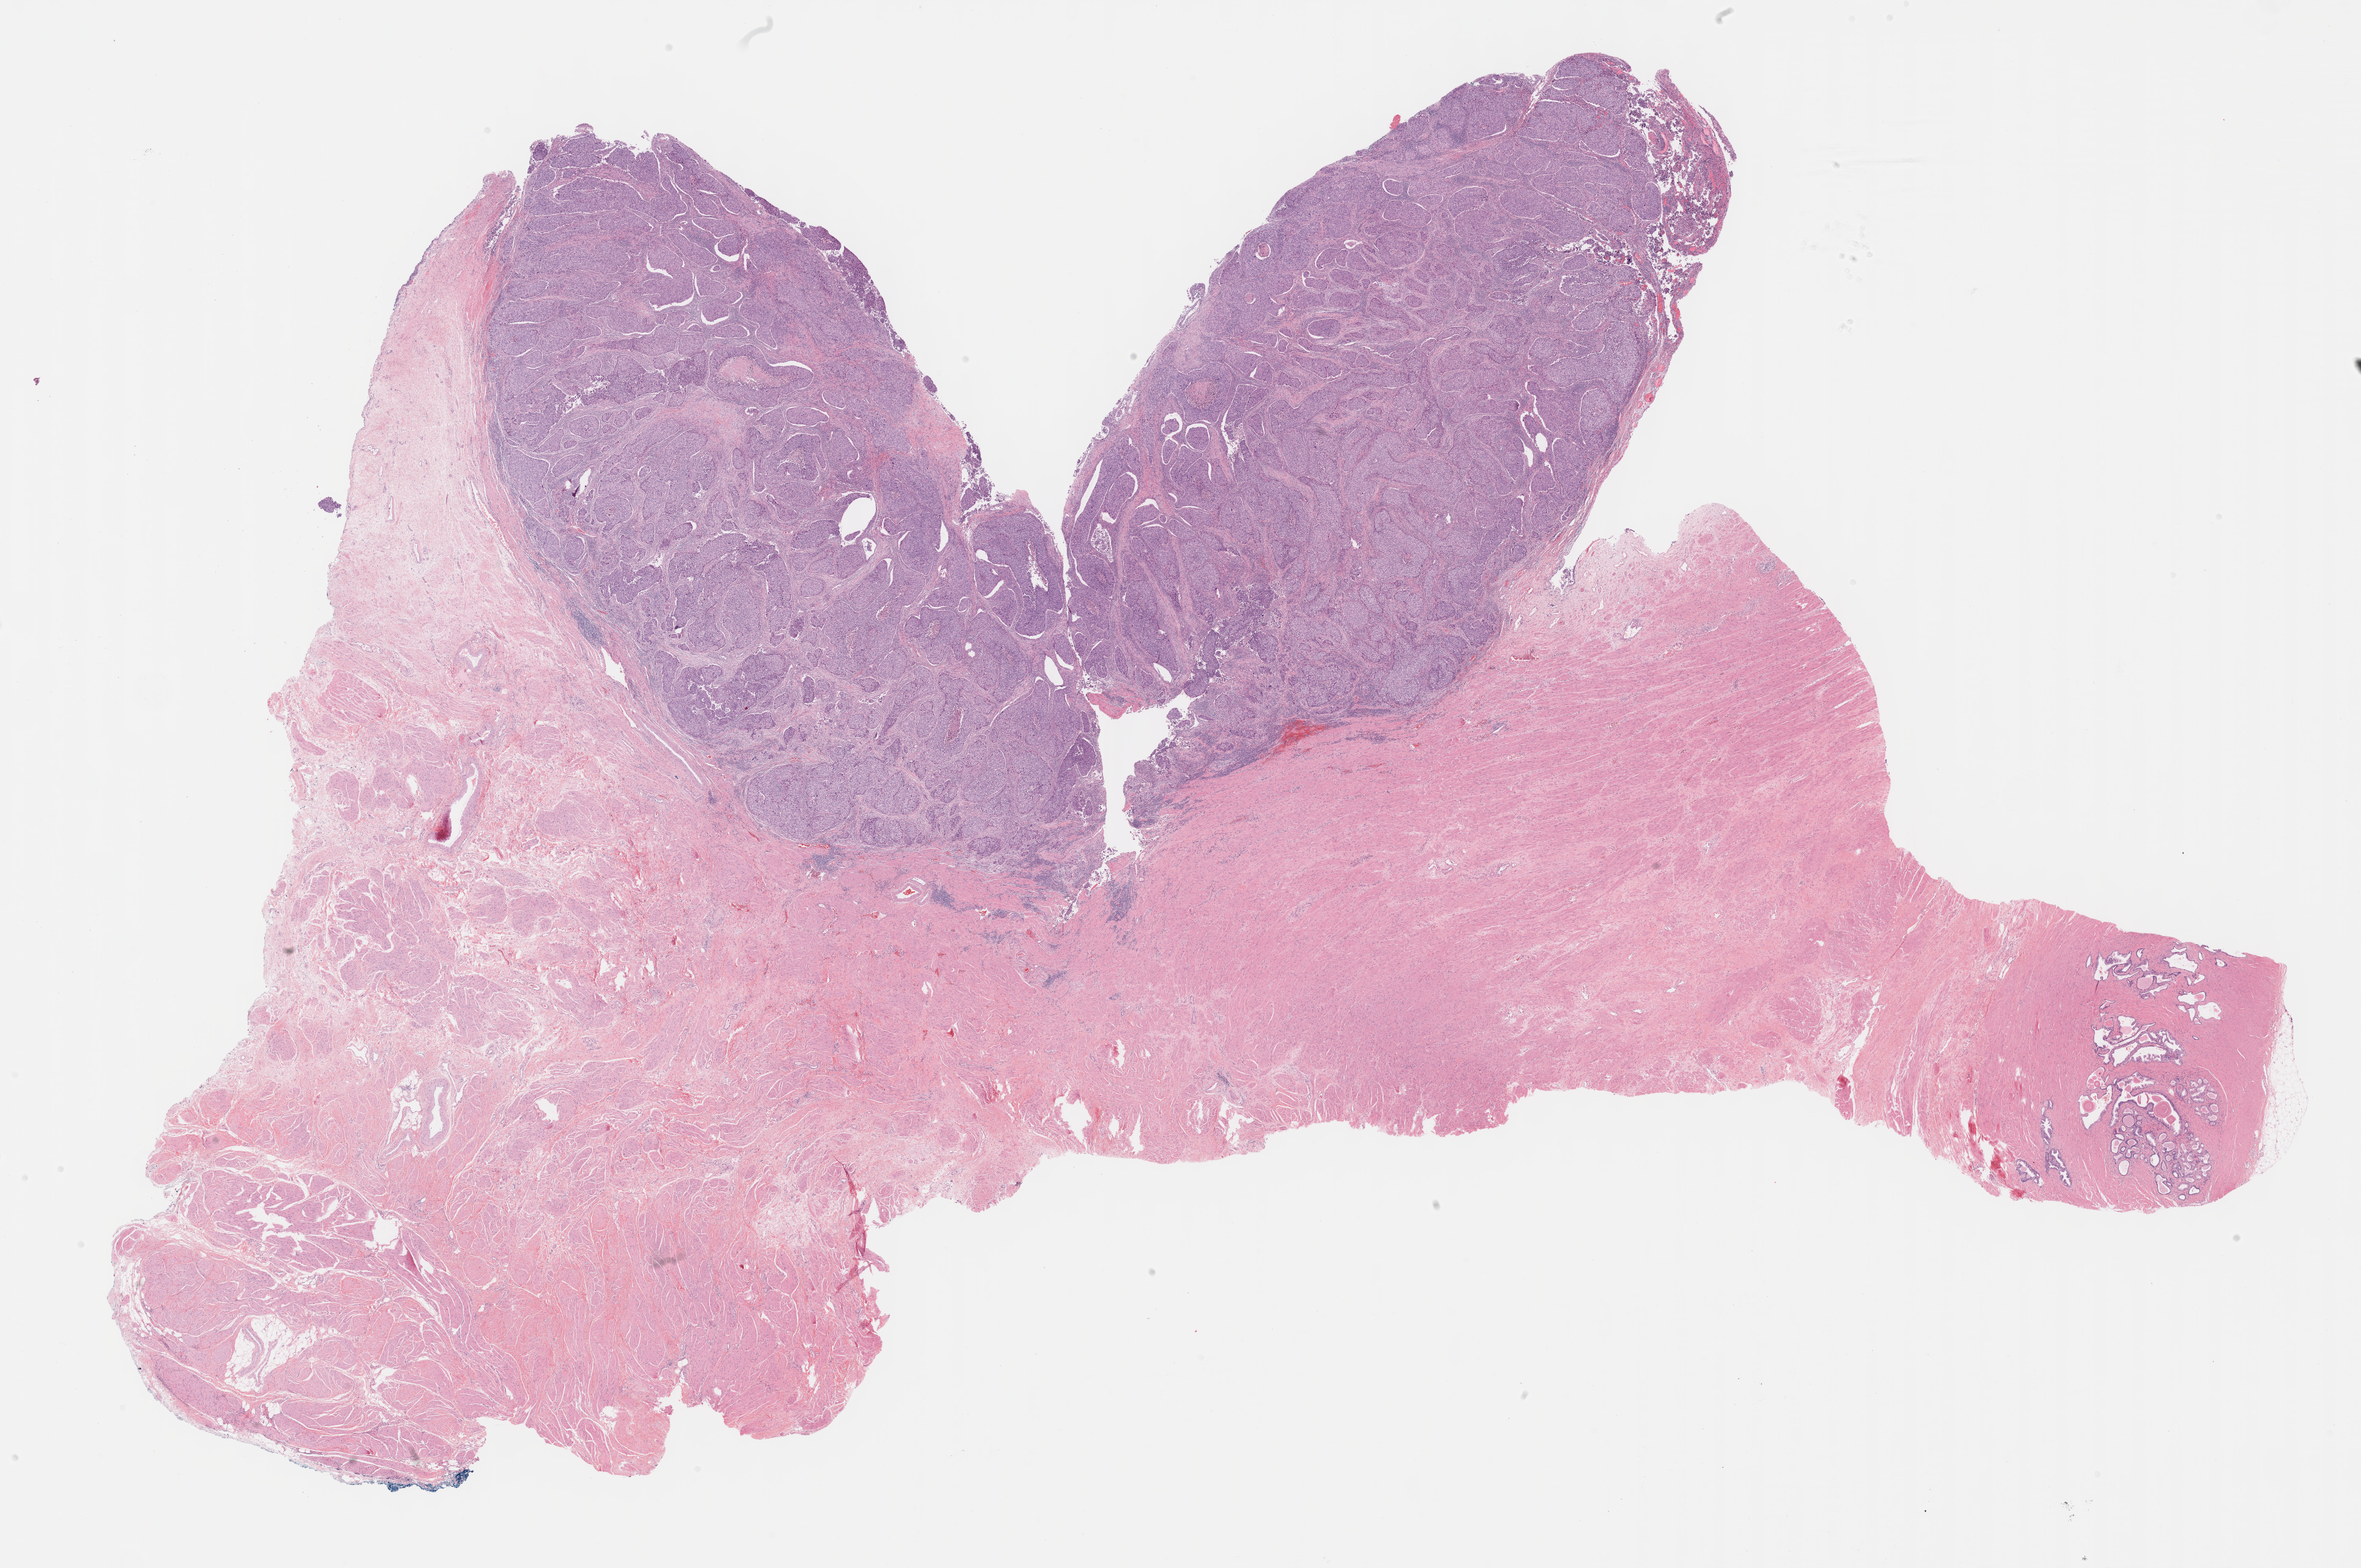
Digitized H&E-stained tissue section (whole slide), low-resolution overview of the scanned area, about 31.2 x 20.7 mm, FFPE section, sample: primary tumour, bladder. Male, age 72 years at initial diagnosis. Histologic grade: high grade.
TNM: T2b N0 MX. AJCC pathologic stage: II (7th edition). Histologic diagnosis: Transitional cell carcinoma.